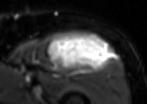
MRI of an extremity soft-tissue mass, one axial slice; slice 68 of 85 in the series (ordered by position); T2-weighted fat-saturated; MR volume resampled by the dataset authors to the PET/CT grid (not the native acquisition matrix); 3.27 mm slice thickness; 147 × 104 image matrix, field of view 144 × 102 mm. Male patient. Case-level facts recorded for this patient, not image findings: histological type: extraskeletal osteosarcoma; grade: high; site of the primary tumour: thigh.
Structures marked on this image (expert contour drawn on MRI and transferred to this co-registered scan by the dataset authors):
- gross tumour volume (mass): bounding box (x1, y1, x2, y2) in pixels: (46, 35, 111, 72)